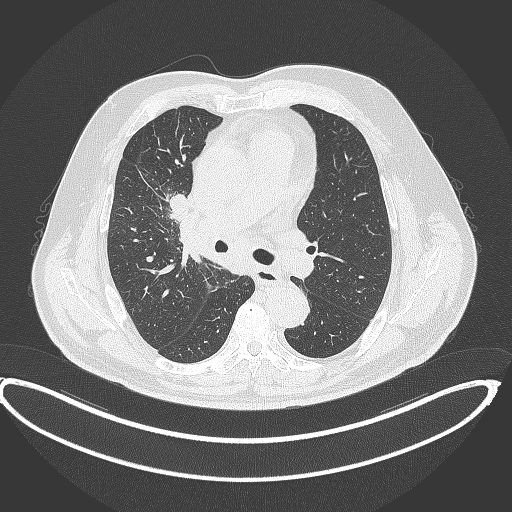
Chest CT, one axial slice. Position 247 of 390 along the scan axis. Reconstruction kernel B70f. 120 kVp. Lung window (W 1500 / L -600 HU). 1 mm slice thickness. 512 × 512 image matrix, field of view 448 × 448 mm. Patient: male, 62 years. From the clinical record (not read from this slice): clinical TNM (as recorded): T1c N3 M1c.
Structures marked on this image (rectangle marked by the reading radiologist):
- lung tumour (recorded histology: adenocarcinoma): bounding box [x1, y1, x2, y2] px = [164, 193, 191, 217]